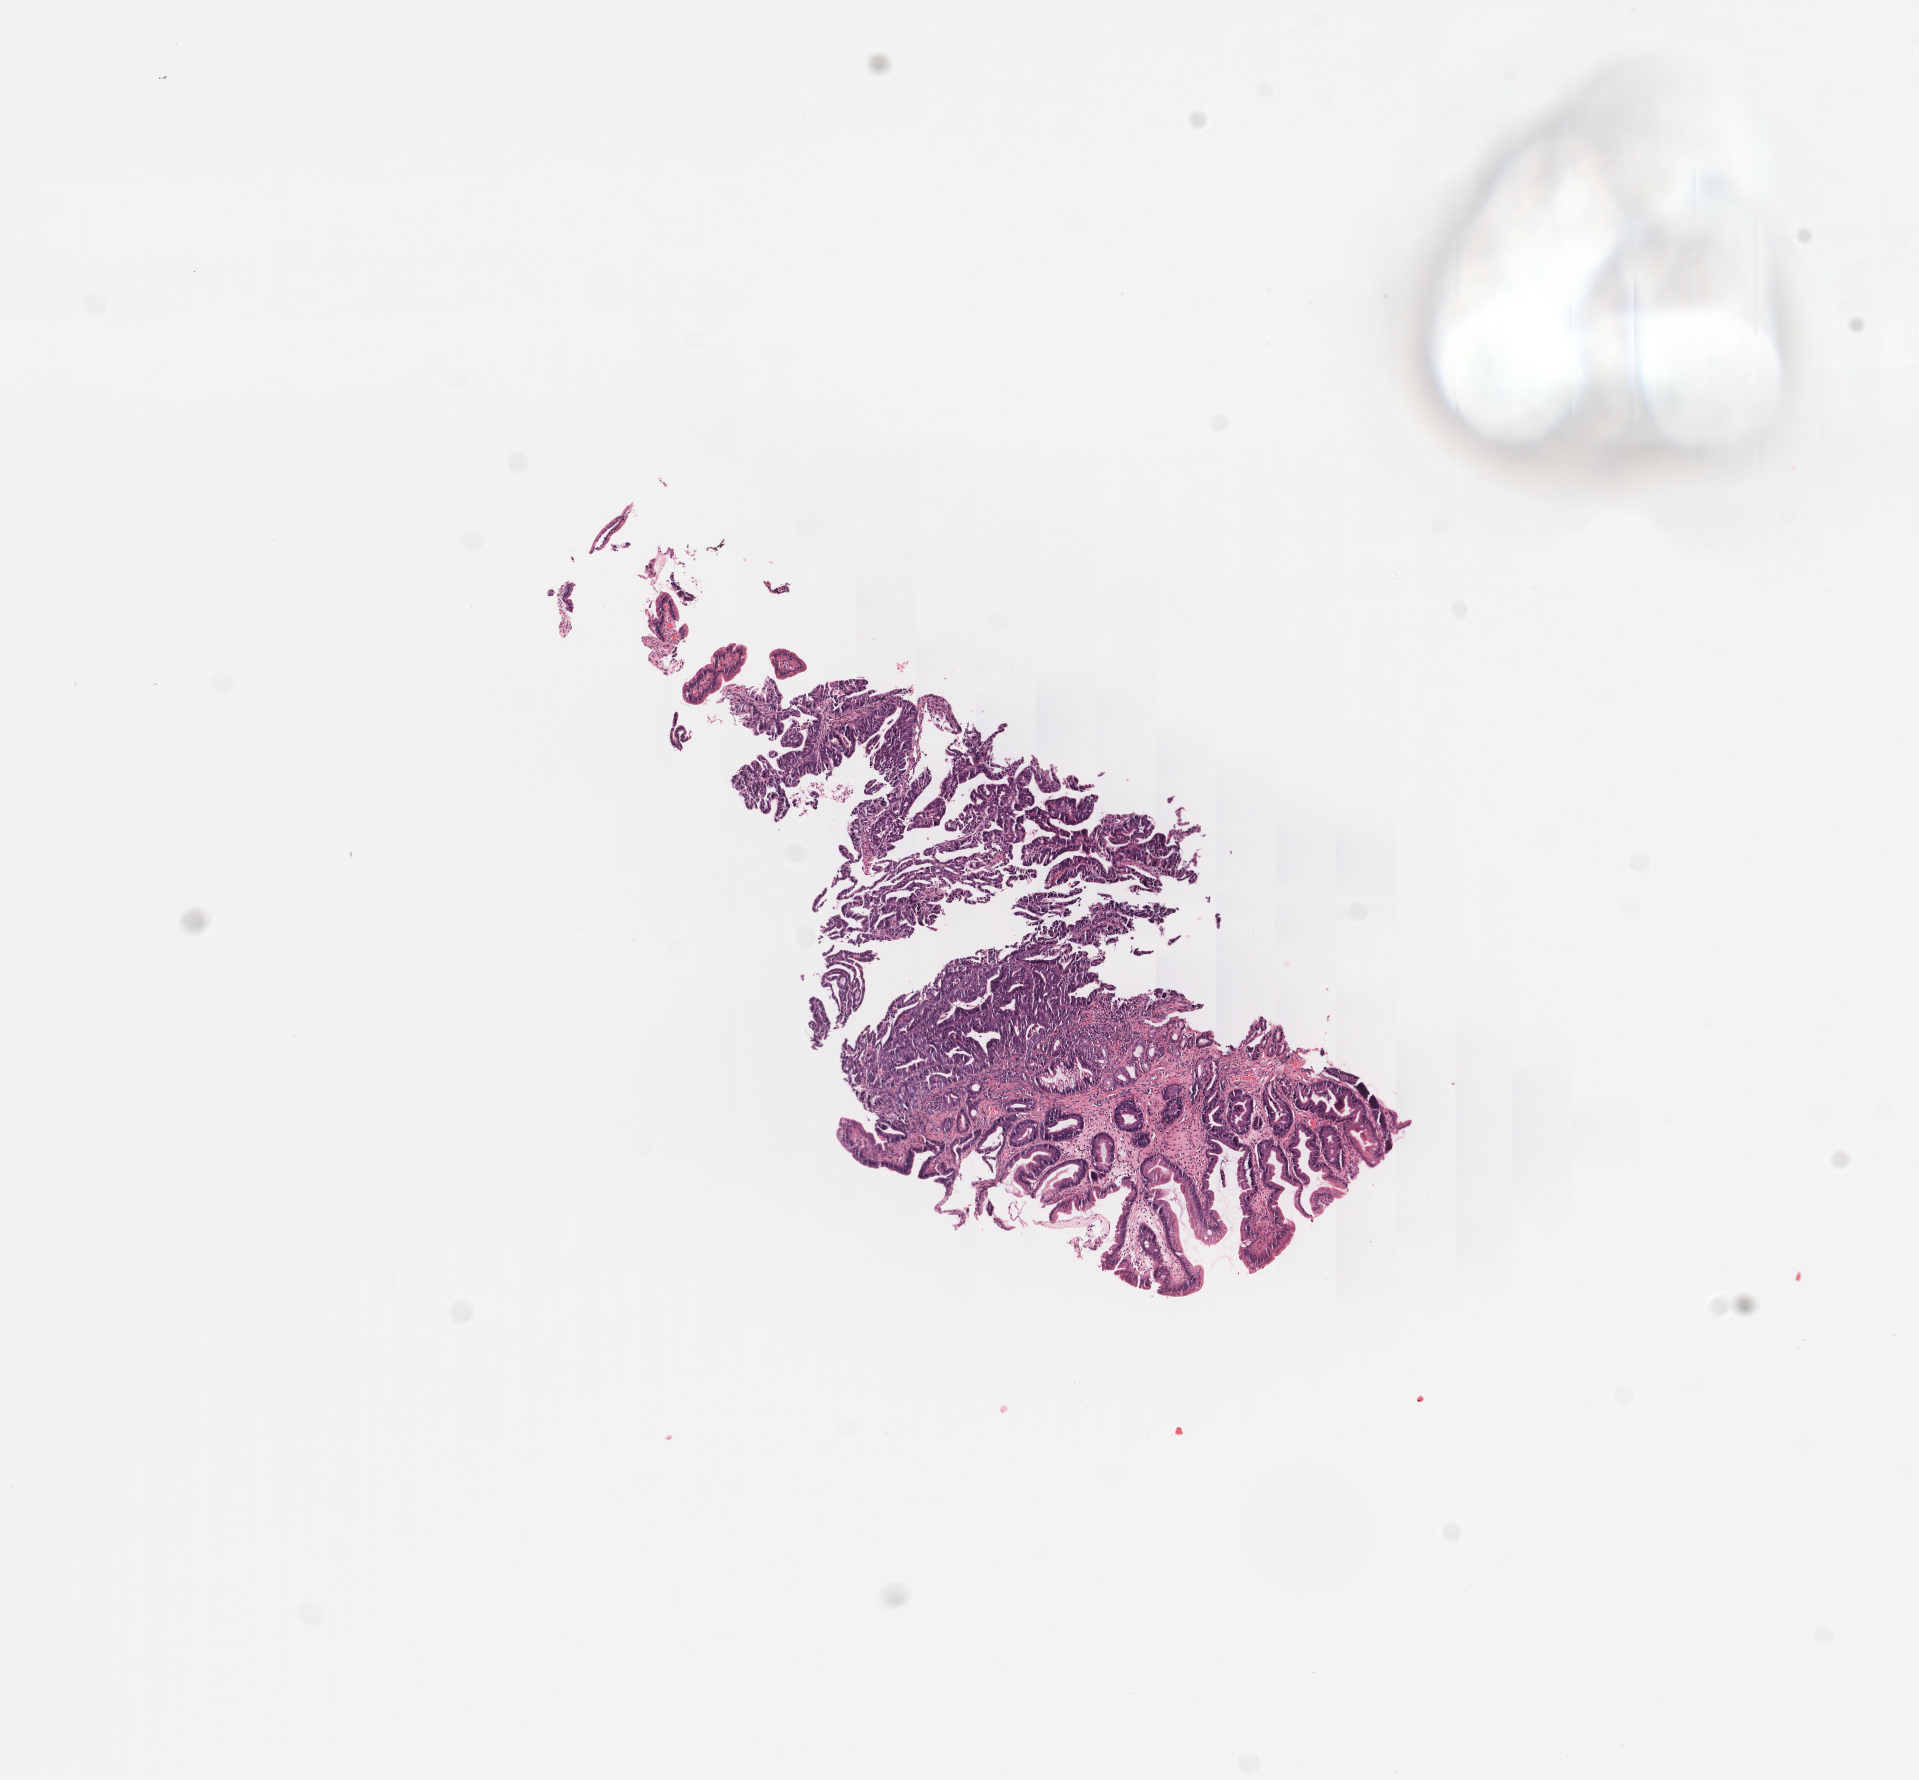
Whole-slide histology image, H&E — shown as a low-resolution overview of the whole scanned area (about 7.7 x 7.2 mm). Formalin-fixed paraffin-embedded (FFPE) diagnostic section. Primary tumour sample from the esophagus. Patient: male, age at initial diagnosis 45 years. Histologic grade: G2 (moderately differentiated).
- lymph nodes positive (case pathology): 1 of 1 examined
- TNM: T1 N0 M0
- histologic diagnosis: Adenocarcinoma, NOS (middle third of esophagus)
- AJCC pathologic stage: IB (7th edition)